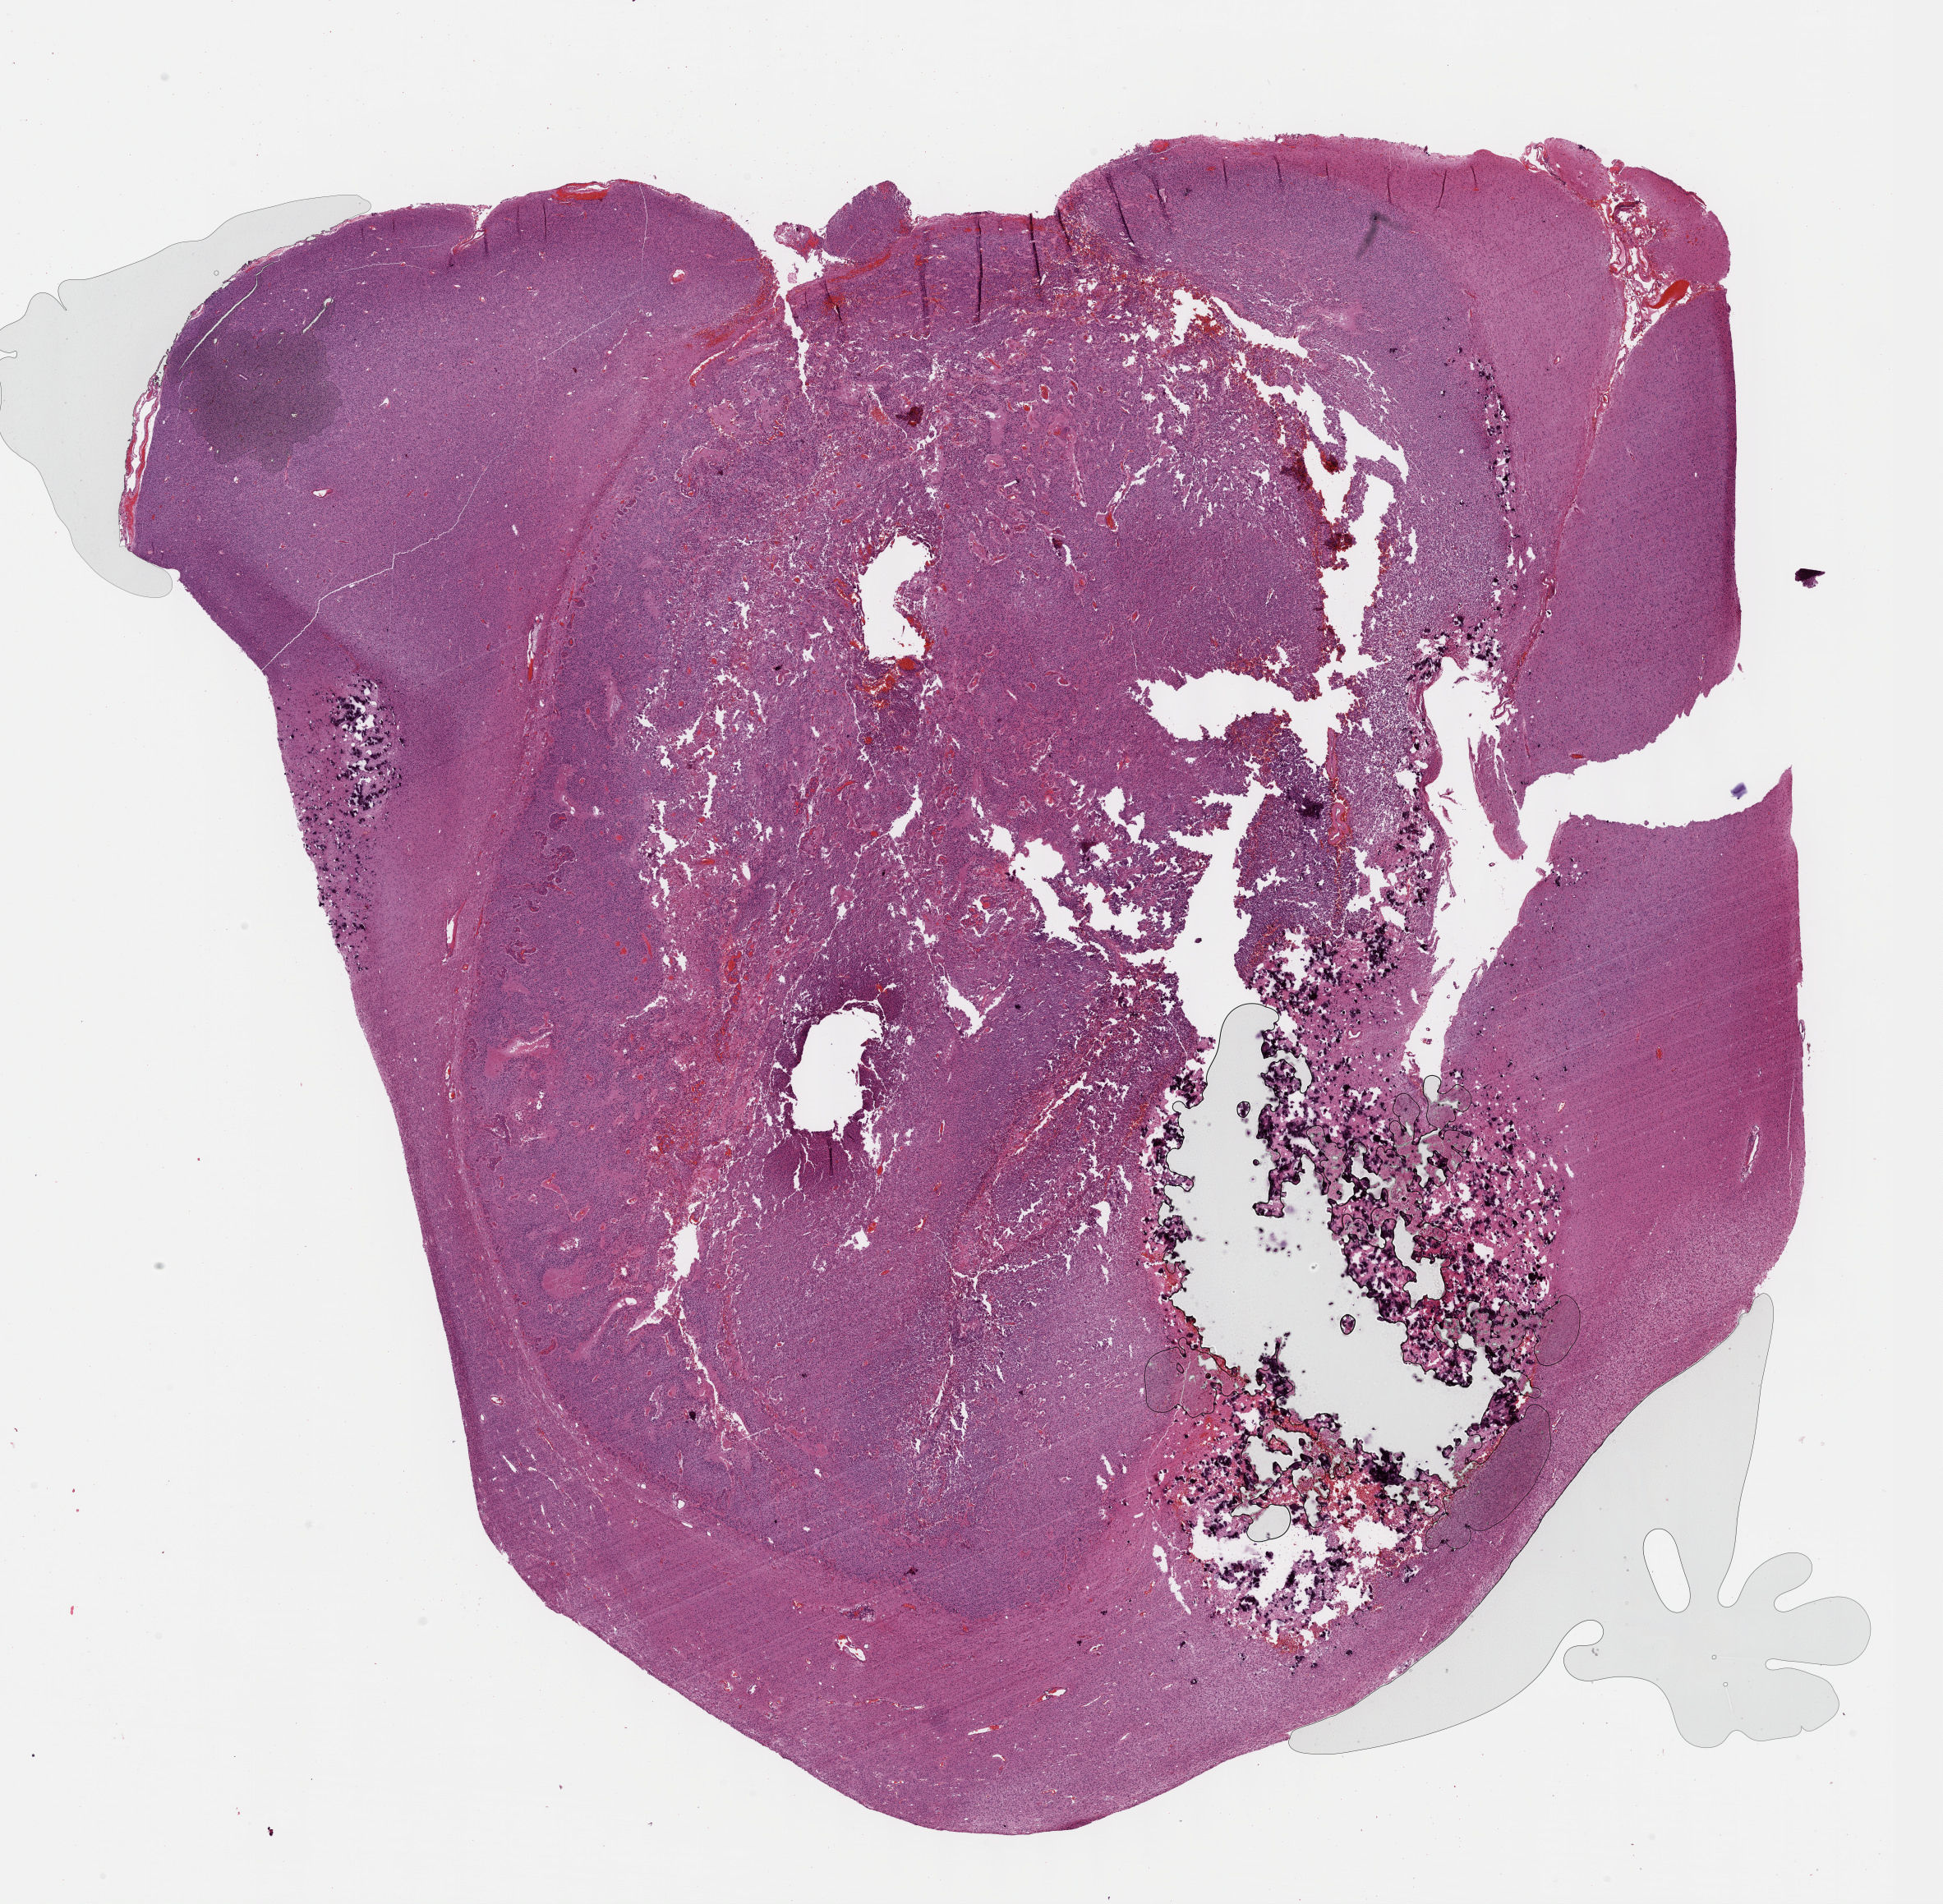
Whole-slide histology image, Hematoxylin and eosin (H&E) stained, a low-resolution overview of the entire scanned area, about 19.1 x 18.7 mm (acquisition: 40x scan); FFPE section; sample: primary tumour, brain. Patient: female, age at initial diagnosis 41 years. Histologic grade: G3 (poorly differentiated).
Pathologic diagnosis: Oligodendroglioma, anaplastic (cerebrum).